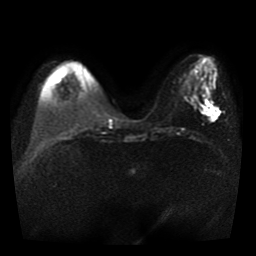
Breast MRI, one axial slice; slice 12 of 41 in the series (ordered by position); diffusion-weighted series; image 2 of 4 stored at this slice position (different b-values; order by instance number); 1.5 T; 256 × 256 image matrix. Female patient.
Annotated regions visible in this slice (expert manual segmentation):
- tumour on diffusion-weighted imaging: bounding box [x1, y1, x2, y2] px = [204, 102, 219, 121]